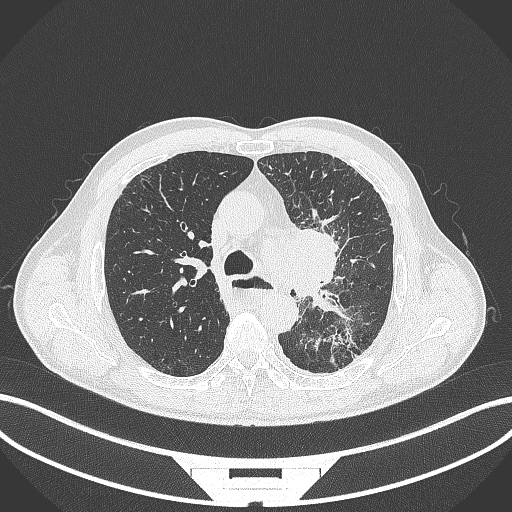
Chest CT, one axial slice. Position 261 of 411 along the scan axis. Reconstruction kernel B70f. Lung window (W 1500 / L -600 HU). 1 mm slice thickness. 512 × 512 image matrix, field of view 400 × 400 mm. Male patient, age 57 years. Case-level facts recorded for this patient, not image findings: clinical TNM (as recorded): T2a N1 M0.
Outlined on this slice (rectangle marked by the reading radiologist):
- lung tumour (recorded histology: squamous cell carcinoma): box from (x=287, y=221) to (x=348, y=309) px